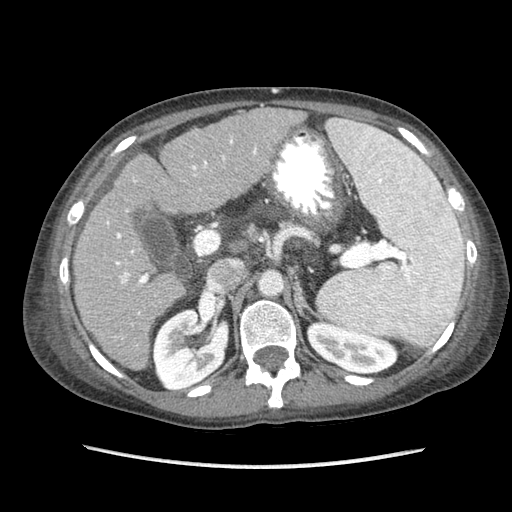
Contrast-enhanced abdominal CT (liver protocol), one axial slice; slice 45 of 87 in the series (ordered by position); reconstruction kernel STANDARD; soft-tissue window (W 400 / L 40 HU); 2.5 mm slice thickness; 512 × 512 image matrix, field of view 340 × 340 mm. Case-level facts recorded for this patient, not image findings: diagnosis: hepatocellular carcinoma (patient treated with transarterial chemoembolisation; whether this scan precedes or follows treatment is not stated here); TNM stage (as recorded): Stage-IIIB; Child-Pugh class: A; tumour differentiation: no biopsy; tumour nodularity: uninodular.
Annotated regions visible in this slice (semi-automatic segmentation, software-assisted and operator-edited):
- liver parenchyma outside the tumour (the mass and vessels are separate outlines, so this box may not span the whole liver): bounding box [x1, y1, x2, y2] px = [72, 108, 306, 370]
- liver vessels: [107, 139, 257, 314]